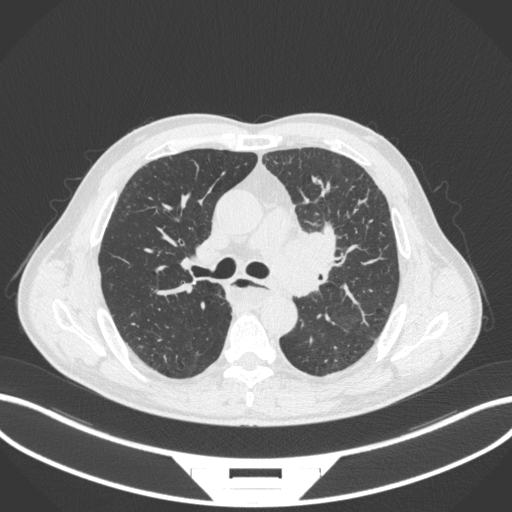
Chest CT, one axial slice; slice 240 of 411 in the series (ordered by position); reconstruction kernel B31f; 120 kVp; lung window (W 1500 / L -600 HU); 1 mm slice thickness; 512 × 512 image matrix, field of view 400 × 400 mm. Patient: male, 57 years. Case-level facts recorded for this patient, not image findings: clinical TNM (as recorded): T2a N1 M0.
Outlined on this slice (bounding box drawn by a radiologist):
- lung tumour (recorded histology: squamous cell carcinoma): box from (x=275, y=224) to (x=340, y=297) px